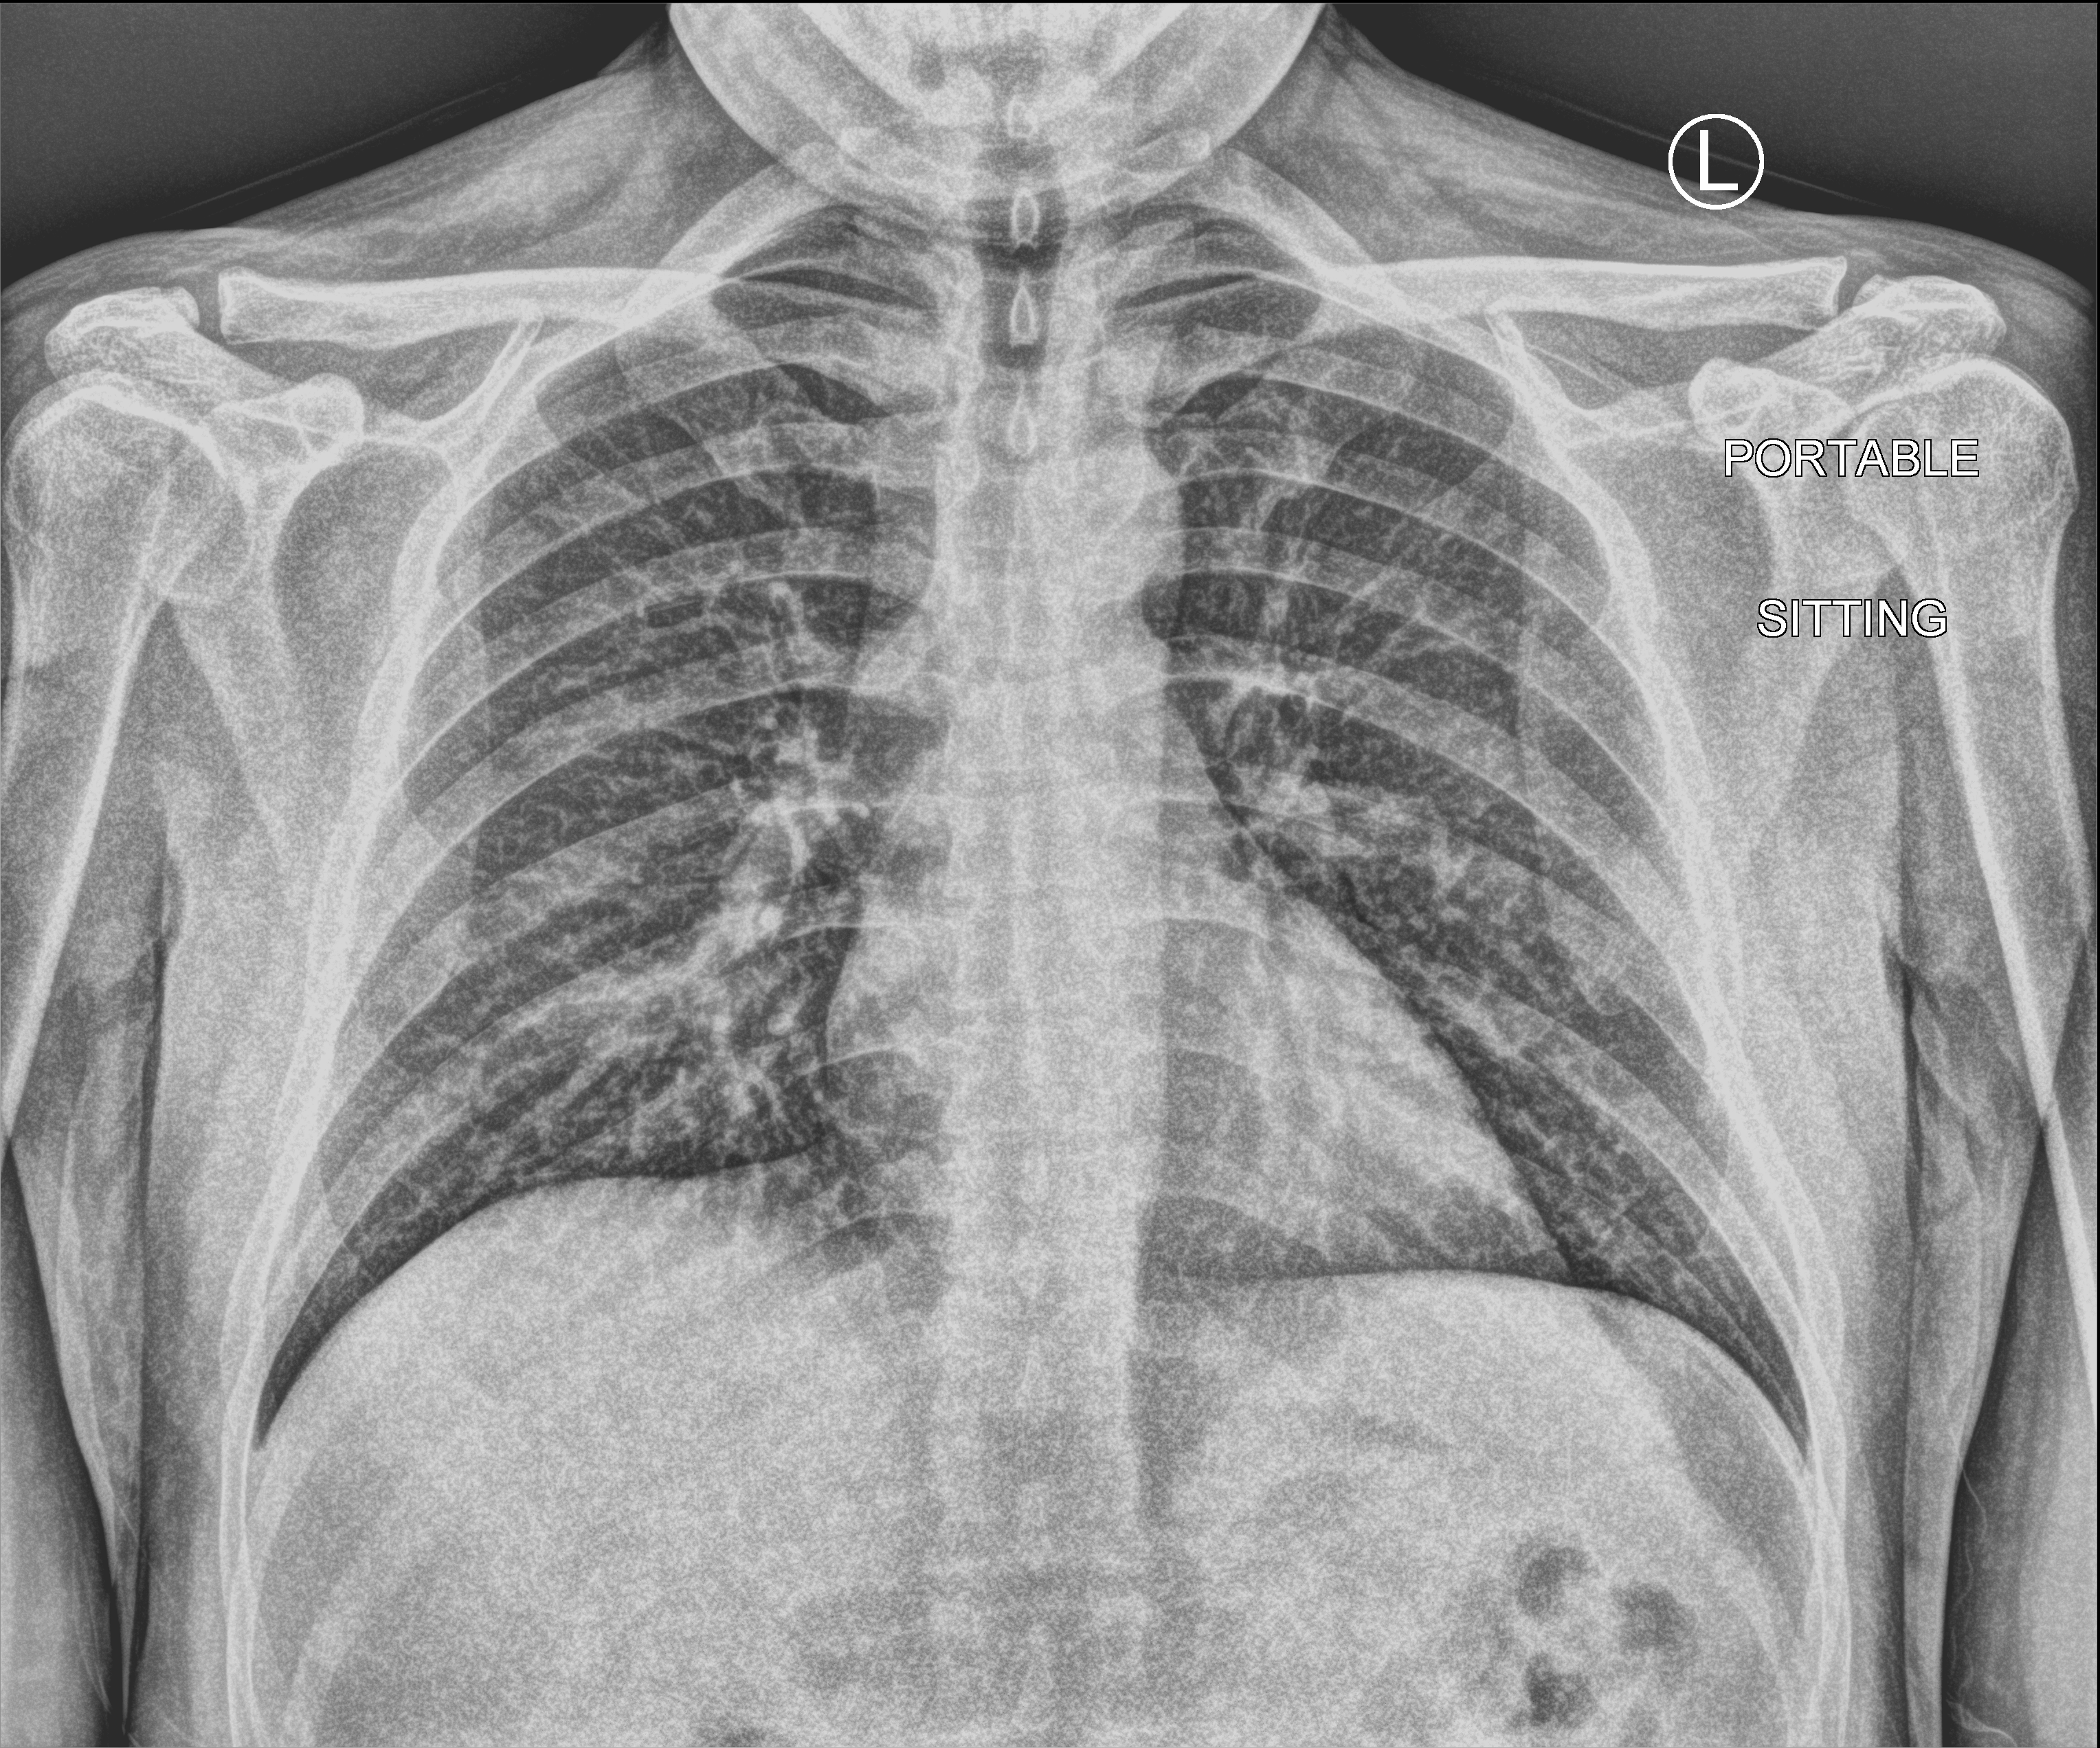
Chest X-ray (portable); anteroposterior (AP) projection. Male patient hospitalised with COVID-19, age 18–59 years.
Admission-level facts for this patient (not findings on this image; timing relative to this image not recorded):
- hypertension (admission record): no